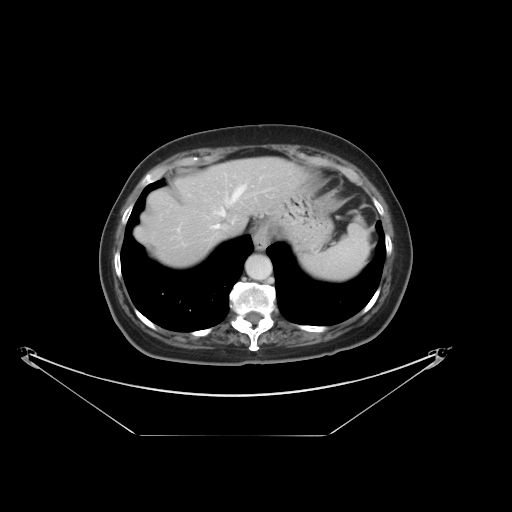
Contrast-enhanced abdominal CT, one axial slice. Slice 30 of 36 in the series (ordered by position). Reconstruction kernel STANDARD. Intravenous contrast given. Soft-tissue window (W 400 / L 40 HU). 5 mm slice thickness. 512 × 512 image matrix, field of view 500 × 500 mm. Female patient, age 70 years. From the clinical record (not read from this slice): diagnosis: colorectal cancer liver metastases, imaged before liver resection; multiple liver metastases: no; largest metastasis: 2.5 cm; chemotherapy before resection: no.
Annotated regions visible in this slice (manually delineated by an expert):
- hepatic veins: bounding box <207,187,245,231> (left, top, right, bottom; pixels)
- liver: <137,158,299,267>
- planned liver remnant (the part of the liver to remain after resection): <136,158,300,267>